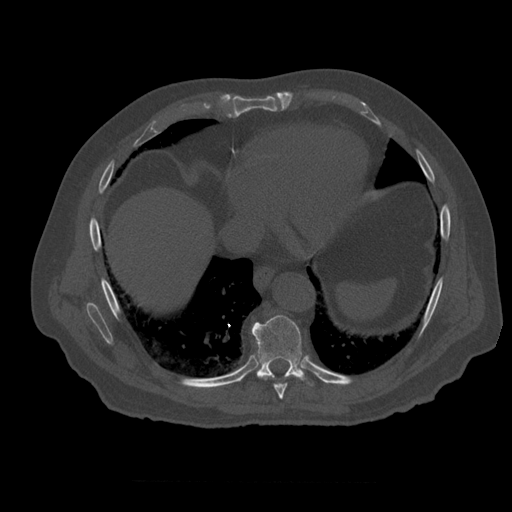
CT including the spine, one axial slice; position 328 of 399 along the scan axis; bone window (W 1800 / L 400 HU); 512 × 512 image matrix, field of view 407 × 407 mm. Patient age 73 years. Case-level facts recorded for this patient, not image findings: primary cancer: prostate; vertebrae with lytic lesions (as recorded): L2.
Structures marked on this image (semi-automatically segmented with operator editing):
- T8 vertebra: bounding box <261,375,289,400> (left, top, right, bottom; pixels)
- T9 vertebra: <252,315,313,386>